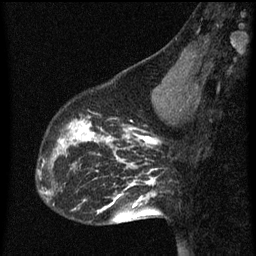
Breast MRI (dynamic contrast-enhanced), one sagittal slice; position 21 of 60 along the scan axis; dynamic contrast-enhanced series, image 2 of 3 at this slice position (ordered by acquisition); 1.5 T; TE 4.2 ms, TR 8 ms; 2 mm slice thickness; 256 × 256 image matrix. Patient: female, 43 years.
Outlined on this slice (semi-automatic segmentation, software-assisted and operator-edited):
- analysis volume of interest (the breast-tissue region the enhancement analysis was run in; not a lesion): bounding box (x1, y1, x2, y2) in pixels: (53, 104, 101, 155)
- tumour enhancement mask (voxels above the 70 % enhancement threshold inside the analysis volume of interest): (54, 120, 101, 155)